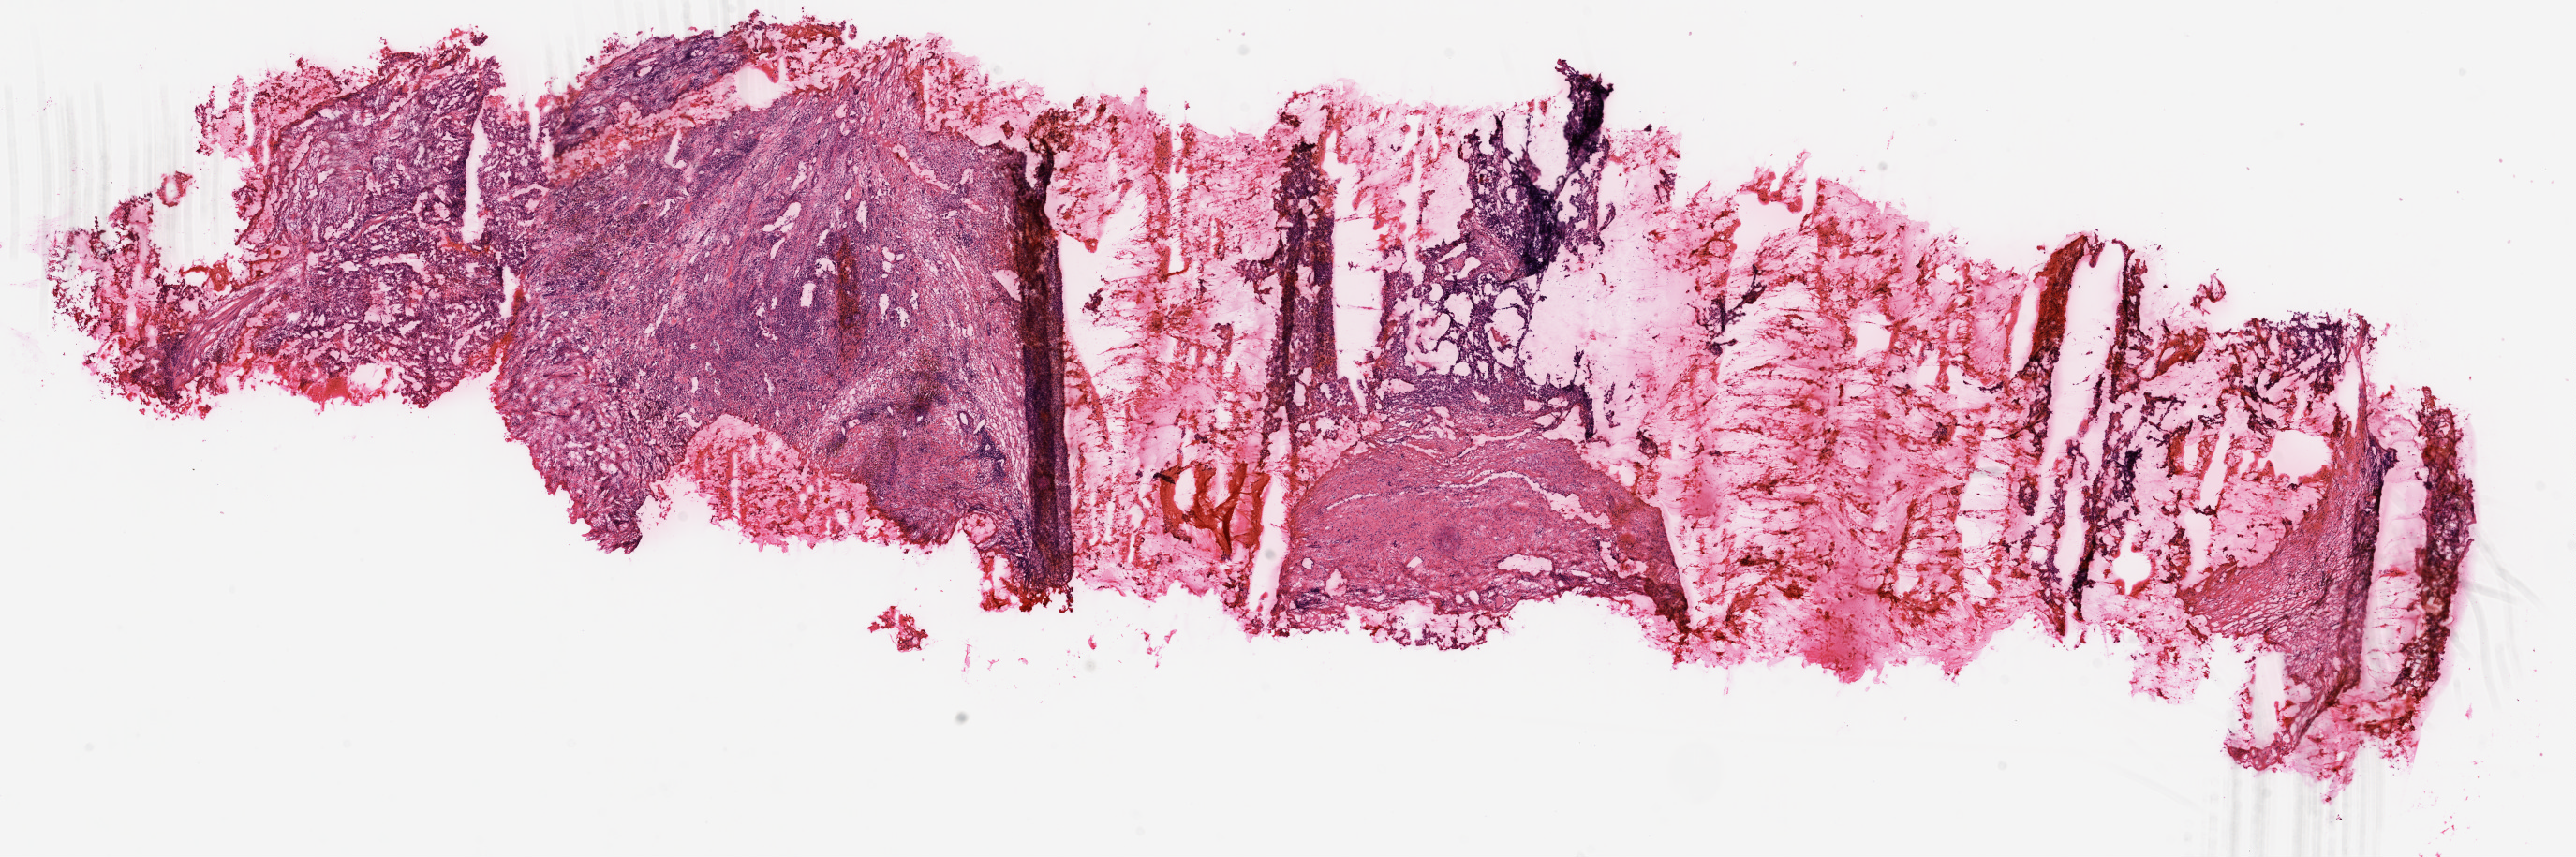
Whole-slide histology image, H&E-stained — low-resolution overview of the scanned area, about 22.1 x 7.3 mm (from a 20x scan). Frozen section from the top of the tissue portion. Primary tumour sample from the kidney. Male, age 72 years at initial diagnosis. Slide review estimates, as recorded: tumour cells 85%, tumour nuclei 75%.
Histologic diagnosis: Clear cell adenocarcinoma, NOS.